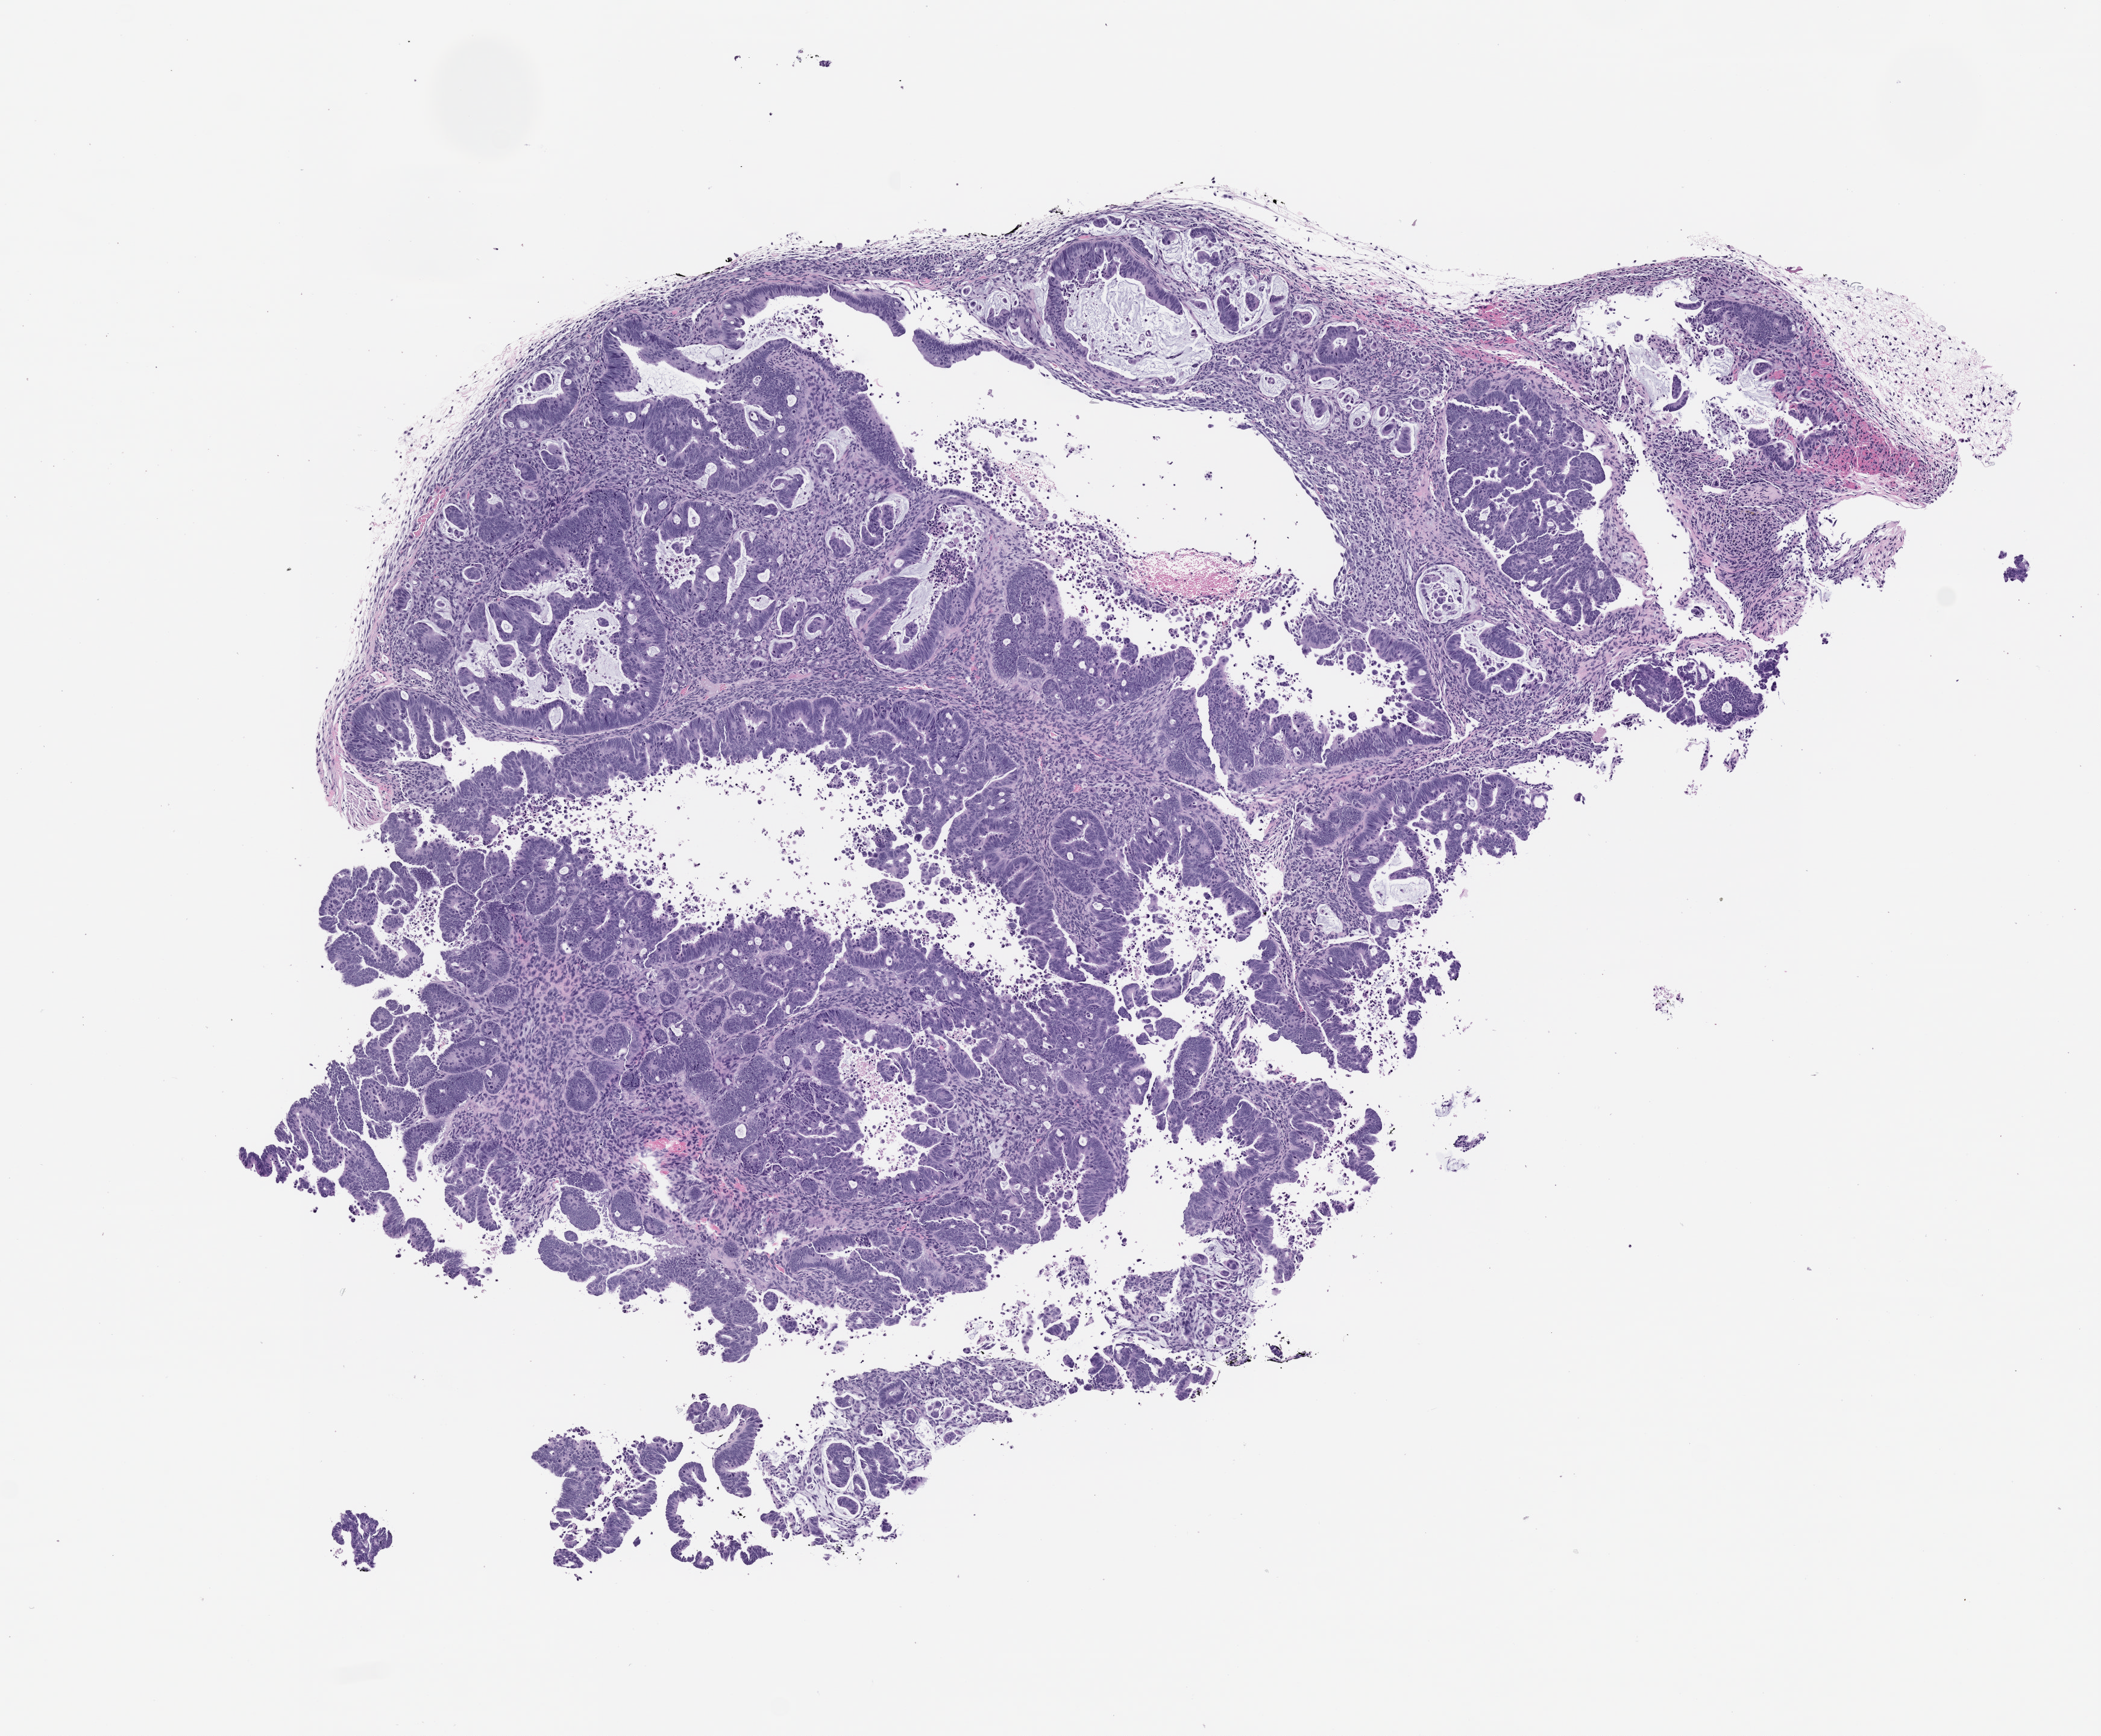
Whole-slide image, haematoxylin and eosin: patient-derived xenograft (human tumor grown in a mouse), passage 1 — whole scanned area (about 7.0 x 5.8 mm) shown as a low-resolution overview. Formalin-fixed, paraffin-embedded (FFPE) tissue. Tumor site category: colon.
- originating patient diagnosis: Colon Adenocarcinoma